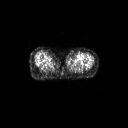
FDG PET of an extremity soft-tissue mass (from a PET/CT study), one axial slice. Slice 55 of 91 in the series (ordered by position). 3.27 mm slice thickness. 128 × 128 image matrix. Patient: female, 74 years. Case-level facts recorded for this patient, not image findings: histological type: pleomorphic leiomyosarcoma; grade: high; site of the primary tumour: left thigh.
Structures marked on this image (expert contour drawn on MRI and transferred to this co-registered scan by the dataset authors):
- gross tumour volume including surrounding oedema: bounding box [x1, y1, x2, y2] px = [67, 54, 73, 59]